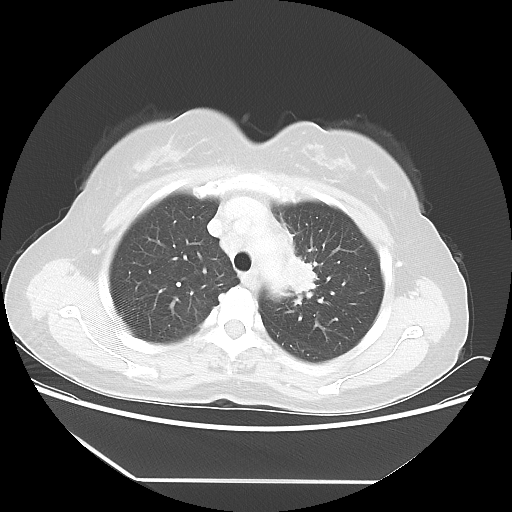
Chest CT, one axial slice; slice 40 of 52 in the series (ordered by position); lung window (W 1500 / L -600 HU); 512 × 512 image matrix. Female patient, age 50 years. Case-level facts recorded for this patient, not image findings: clinical TNM (as recorded): T2 N3 M0.
Outlined on this slice (bounding box drawn by a radiologist):
- lung tumour (recorded histology: adenocarcinoma): bounding box (x1, y1, x2, y2) in pixels: (275, 239, 322, 310)